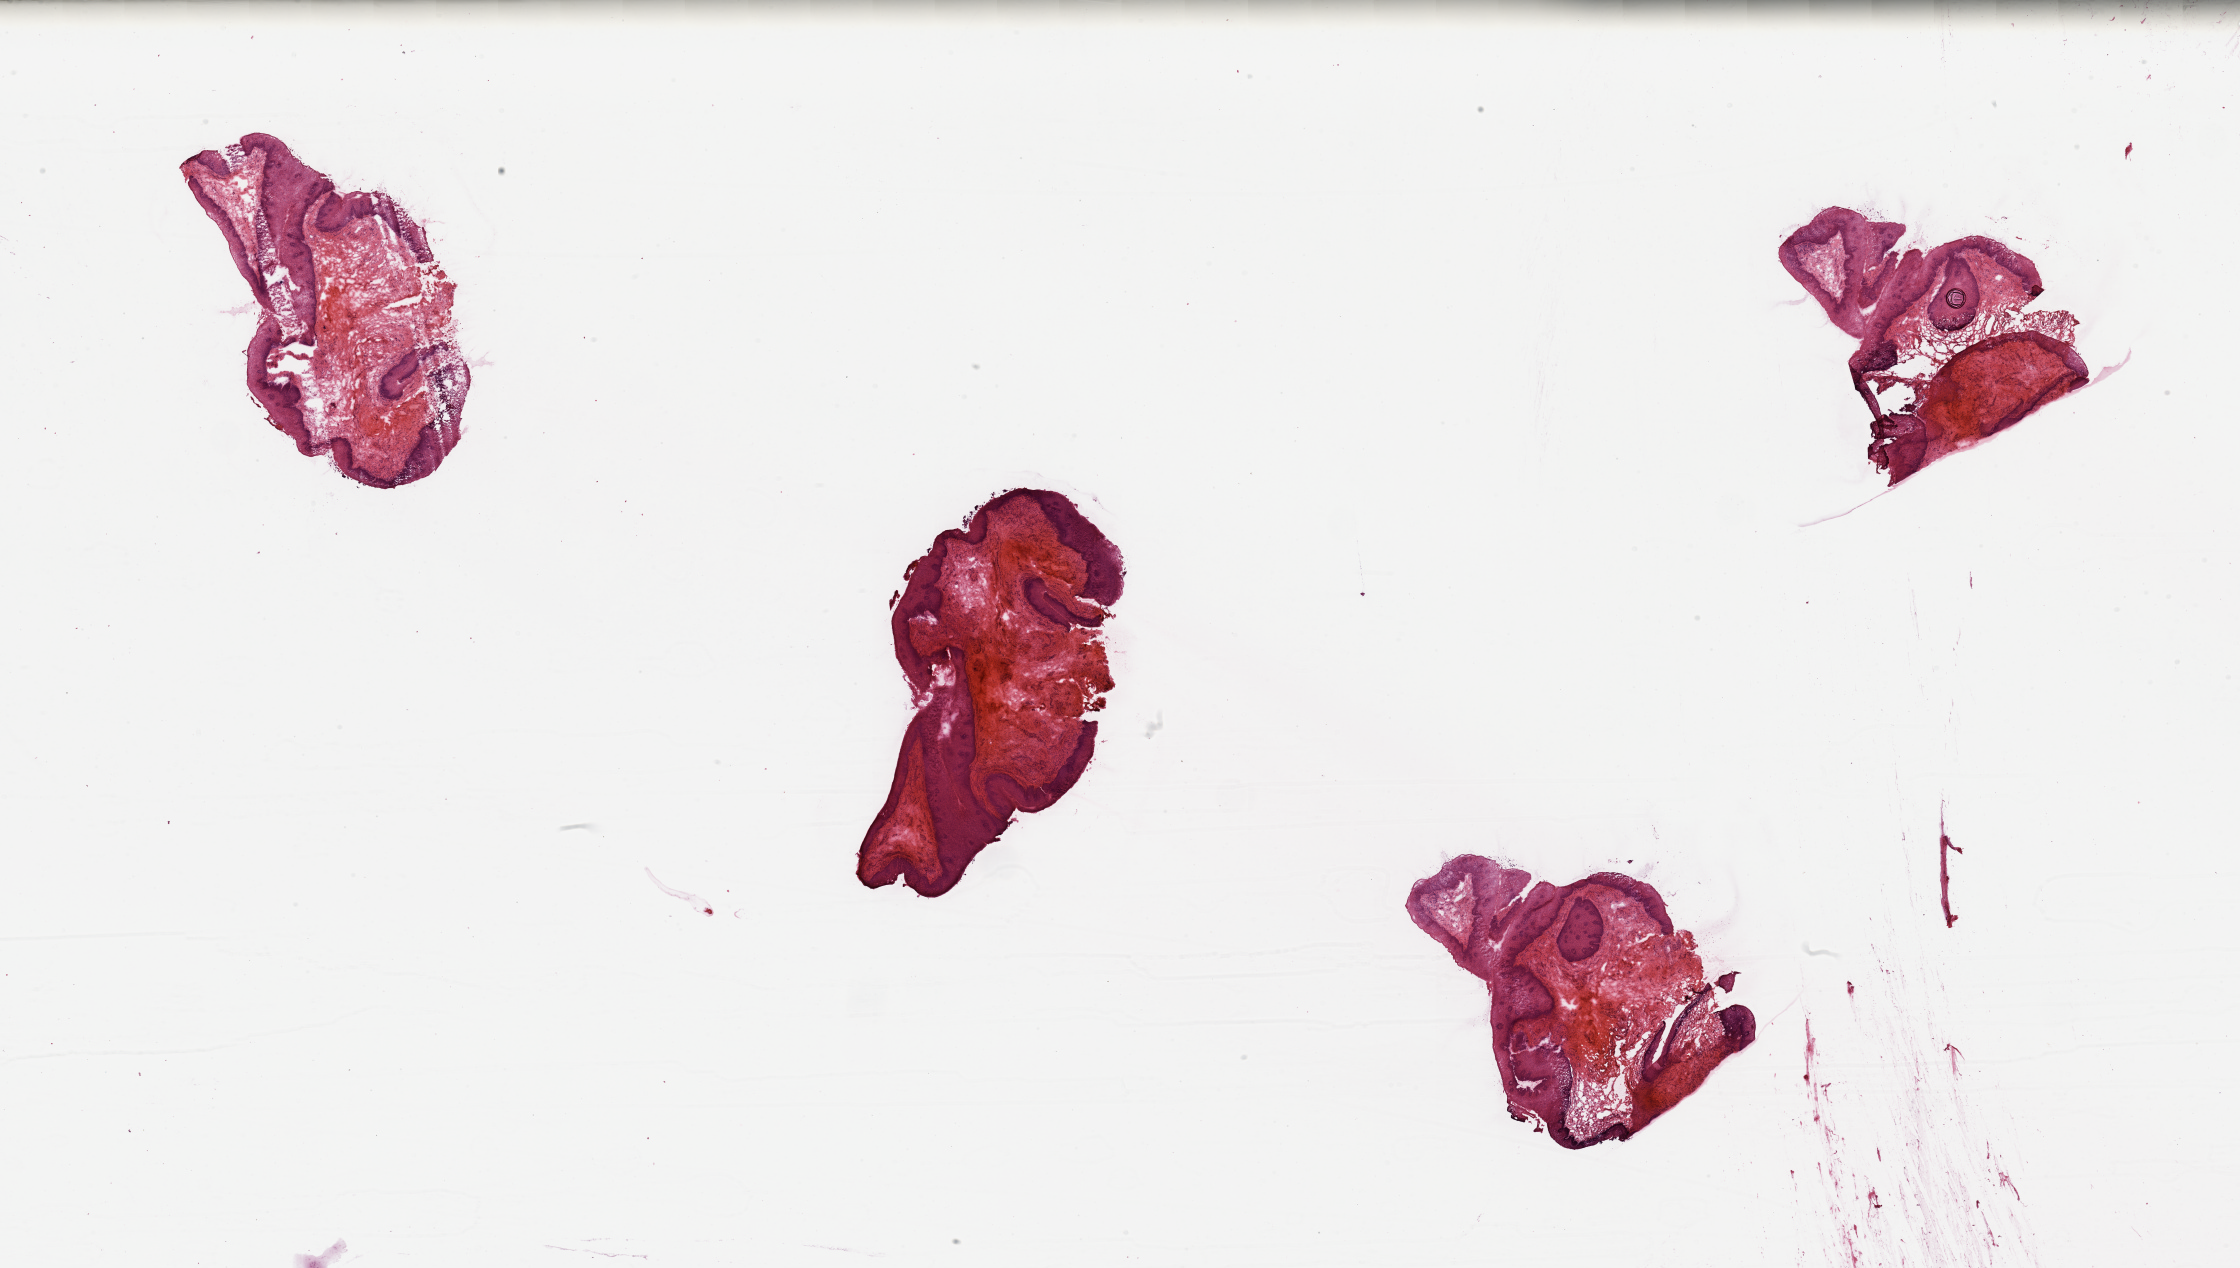
Whole-slide histology image, Hematoxylin and eosin (H&E) stained — whole scanned area (about 35.4 x 20.1 mm) shown as a low-resolution overview. Head and neck, normal (non-tumour) tissue. 53-year-old female patient.
This section: normal (non-tumour) tissue from the same patient. Patient diagnosis: Squamous cell carcinoma, NOS.